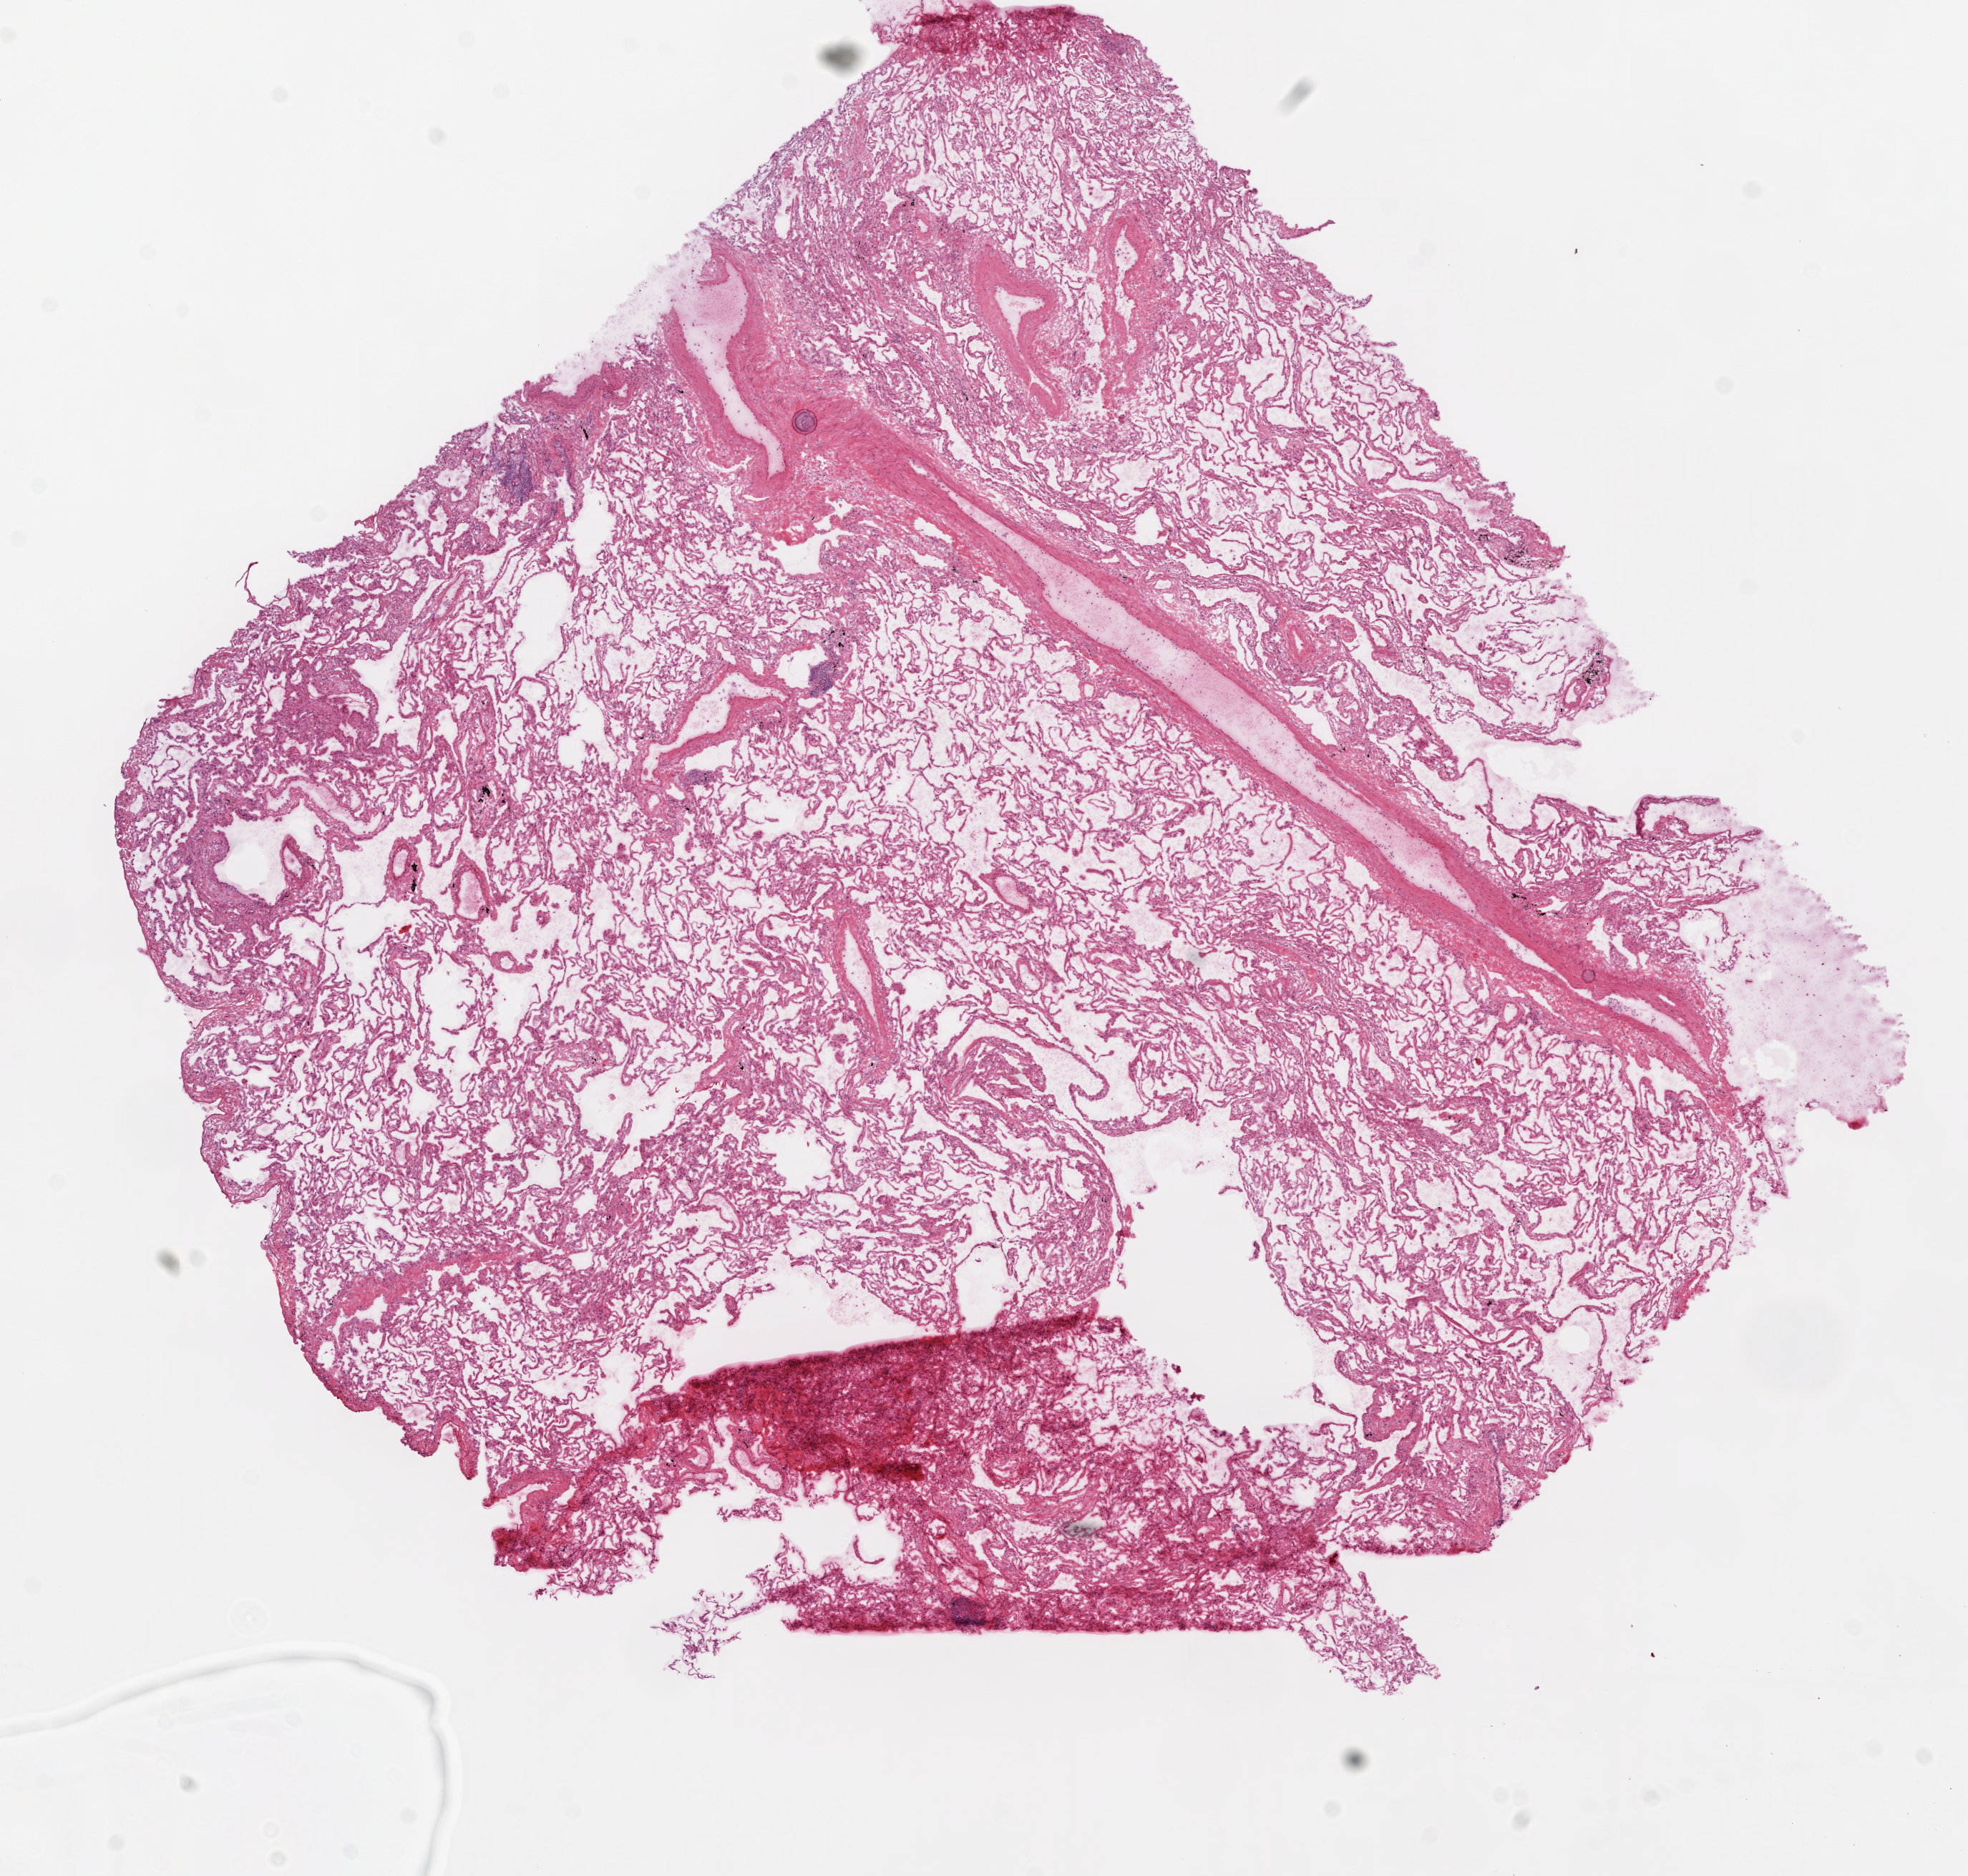
Whole-slide histology image, Hematoxylin and eosin (H&E) stained, whole scanned area (about 11.0 x 10.5 mm, slide scanned at 20x) shown as a low-resolution overview; frozen section; sample: solid tissue normal (non-tumour tissue), lung. Patient: female, age at initial diagnosis 73 years.
This section: solid tissue normal sample (biorepository sample class). Patient diagnosis: Squamous cell carcinoma, NOS (upper lobe, lung).